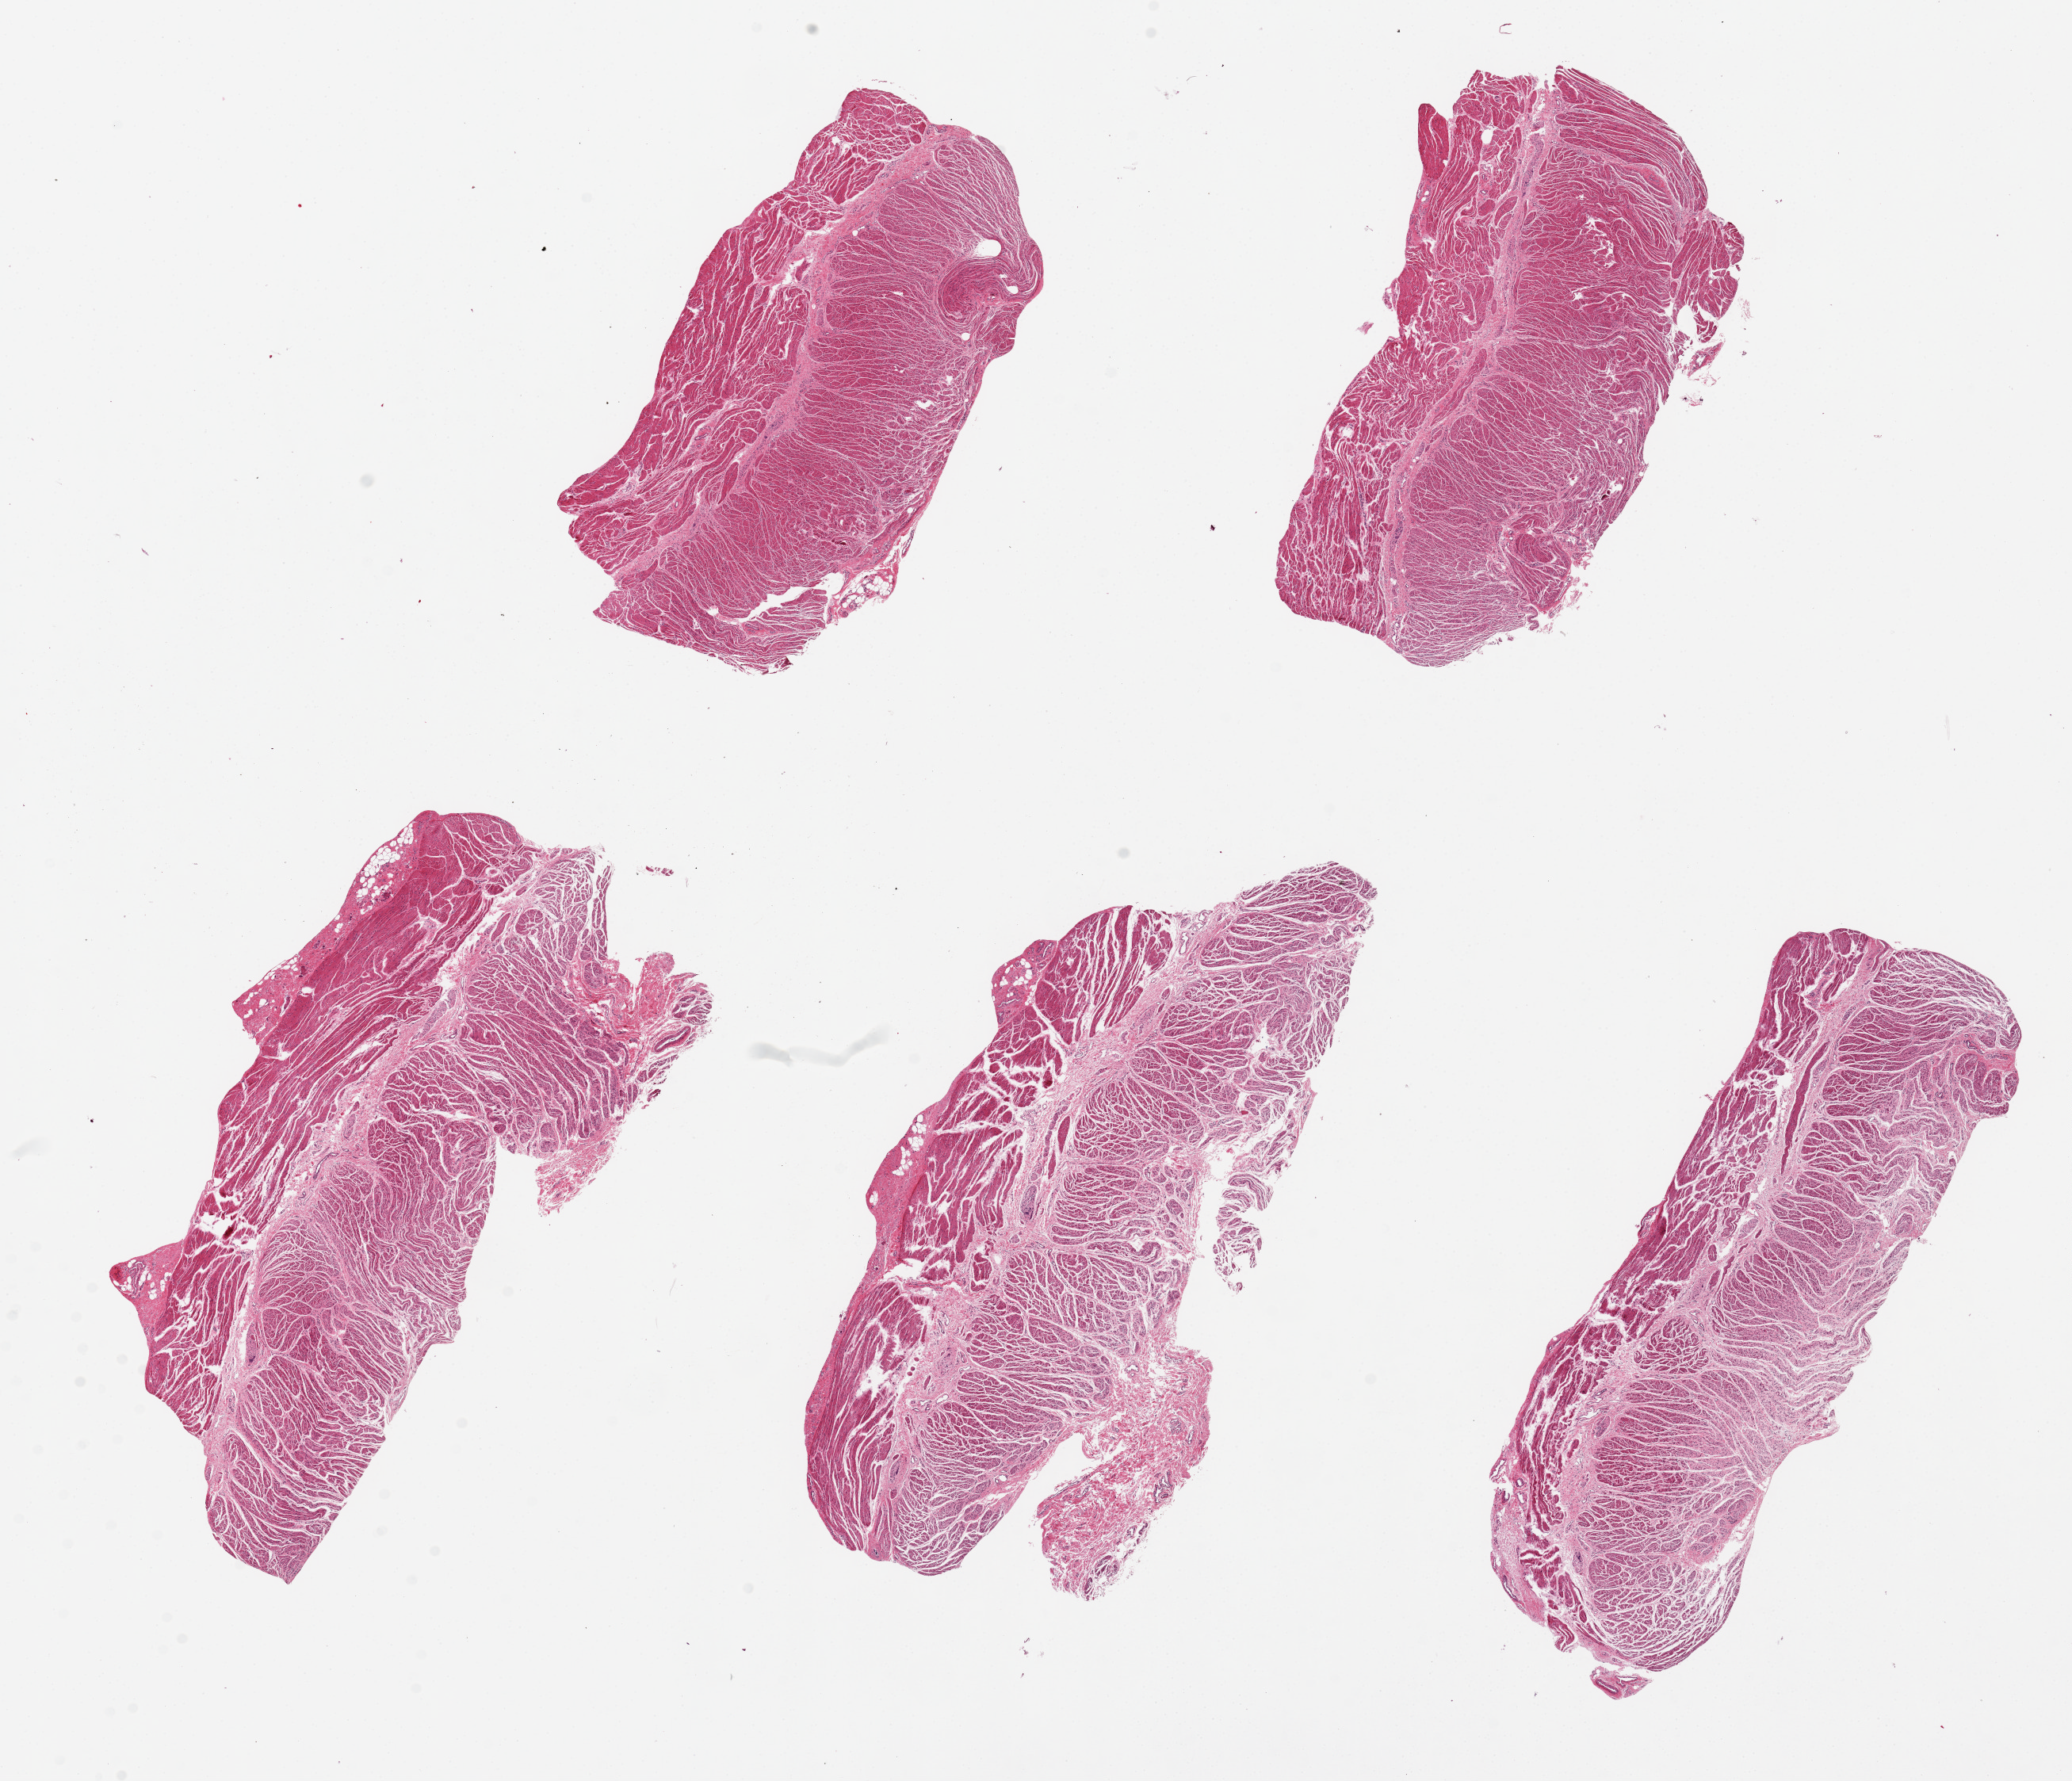
Digitized H&E-stained section, a low-resolution overview of the entire scanned area, about 20.7 x 17.8 mm (slide scanned at 20x); PAXgene-fixed, paraffin-embedded tissue; sampled site (target tissue): gastroesophageal junction; donor tissue sample. Donor: male.
Reviewer comment on this tissue sample: 5 pieces; well trimmed.